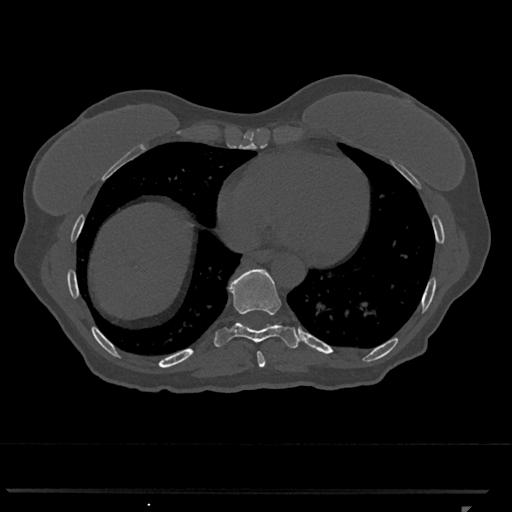
CT including the spine, one axial slice; slice 617 of 793 in the series (ordered by position); 120 kVp; bone window (W 1800 / L 400 HU); 0.5 mm slice thickness; 512 × 512 image matrix. Patient: female, 62 years. From the clinical record (not read from this slice): primary cancer: renal.
Annotated regions visible in this slice (semi-automatic segmentation, software-assisted and operator-edited):
- T8 vertebra: box from (x=257, y=351) to (x=266, y=367) px
- T9 vertebra: (x=214, y=269)–(x=300, y=349)